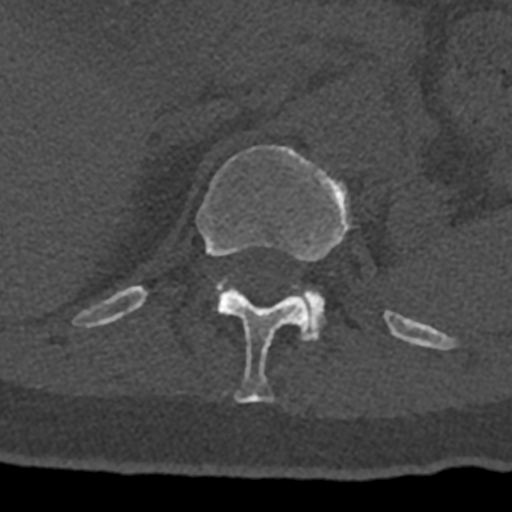
CT including the spine, one axial slice. Position 480 of 797 along the scan axis. Reconstruction kernel Br40s/3. 120 kVp. Bone window (W 1800 / L 400 HU). 512 × 512 image matrix. Patient: male, 74 years. From the clinical record (not read from this slice): primary cancer: renal; vertebrae with lytic lesions (as recorded): T10, L1, L2, L3, L4, L5.
Structures marked on this image (semi-automatically segmented with operator editing):
- L1 vertebra: bounding box <215,279,325,341> (left, top, right, bottom; pixels)
- T12 vertebra: <73,145,432,403>